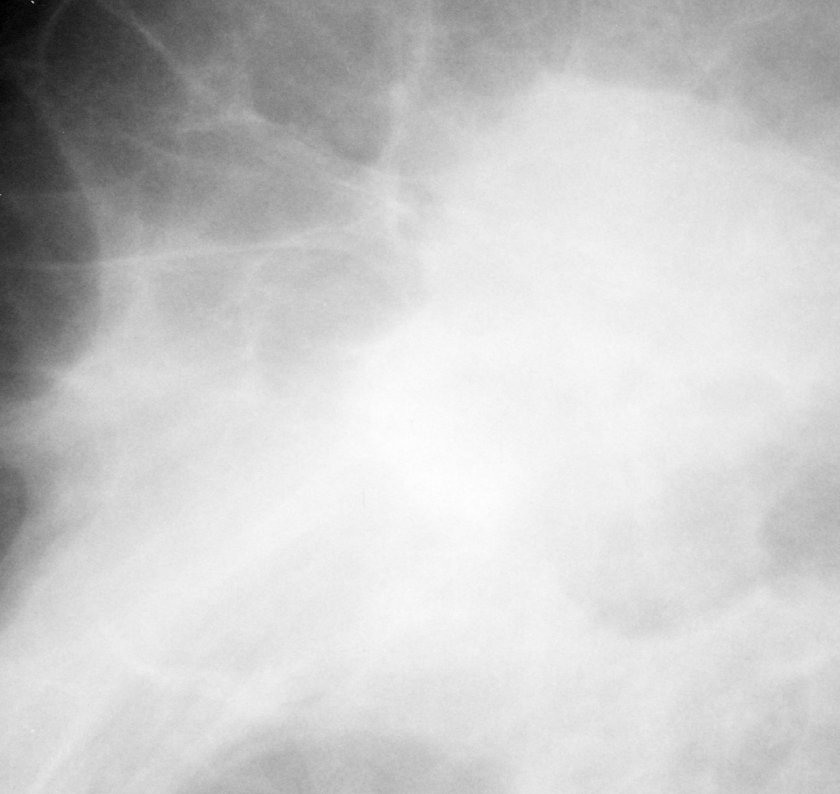
Crop from a digitized film mammogram around one marked abnormality, right breast, MLO view.
Finding: mass, shape irregular / architectural distortion, margins obscured / ill defined / spiculated; BI-RADS assessment category 4; pathology result (as recorded, not read from the image): malignant.